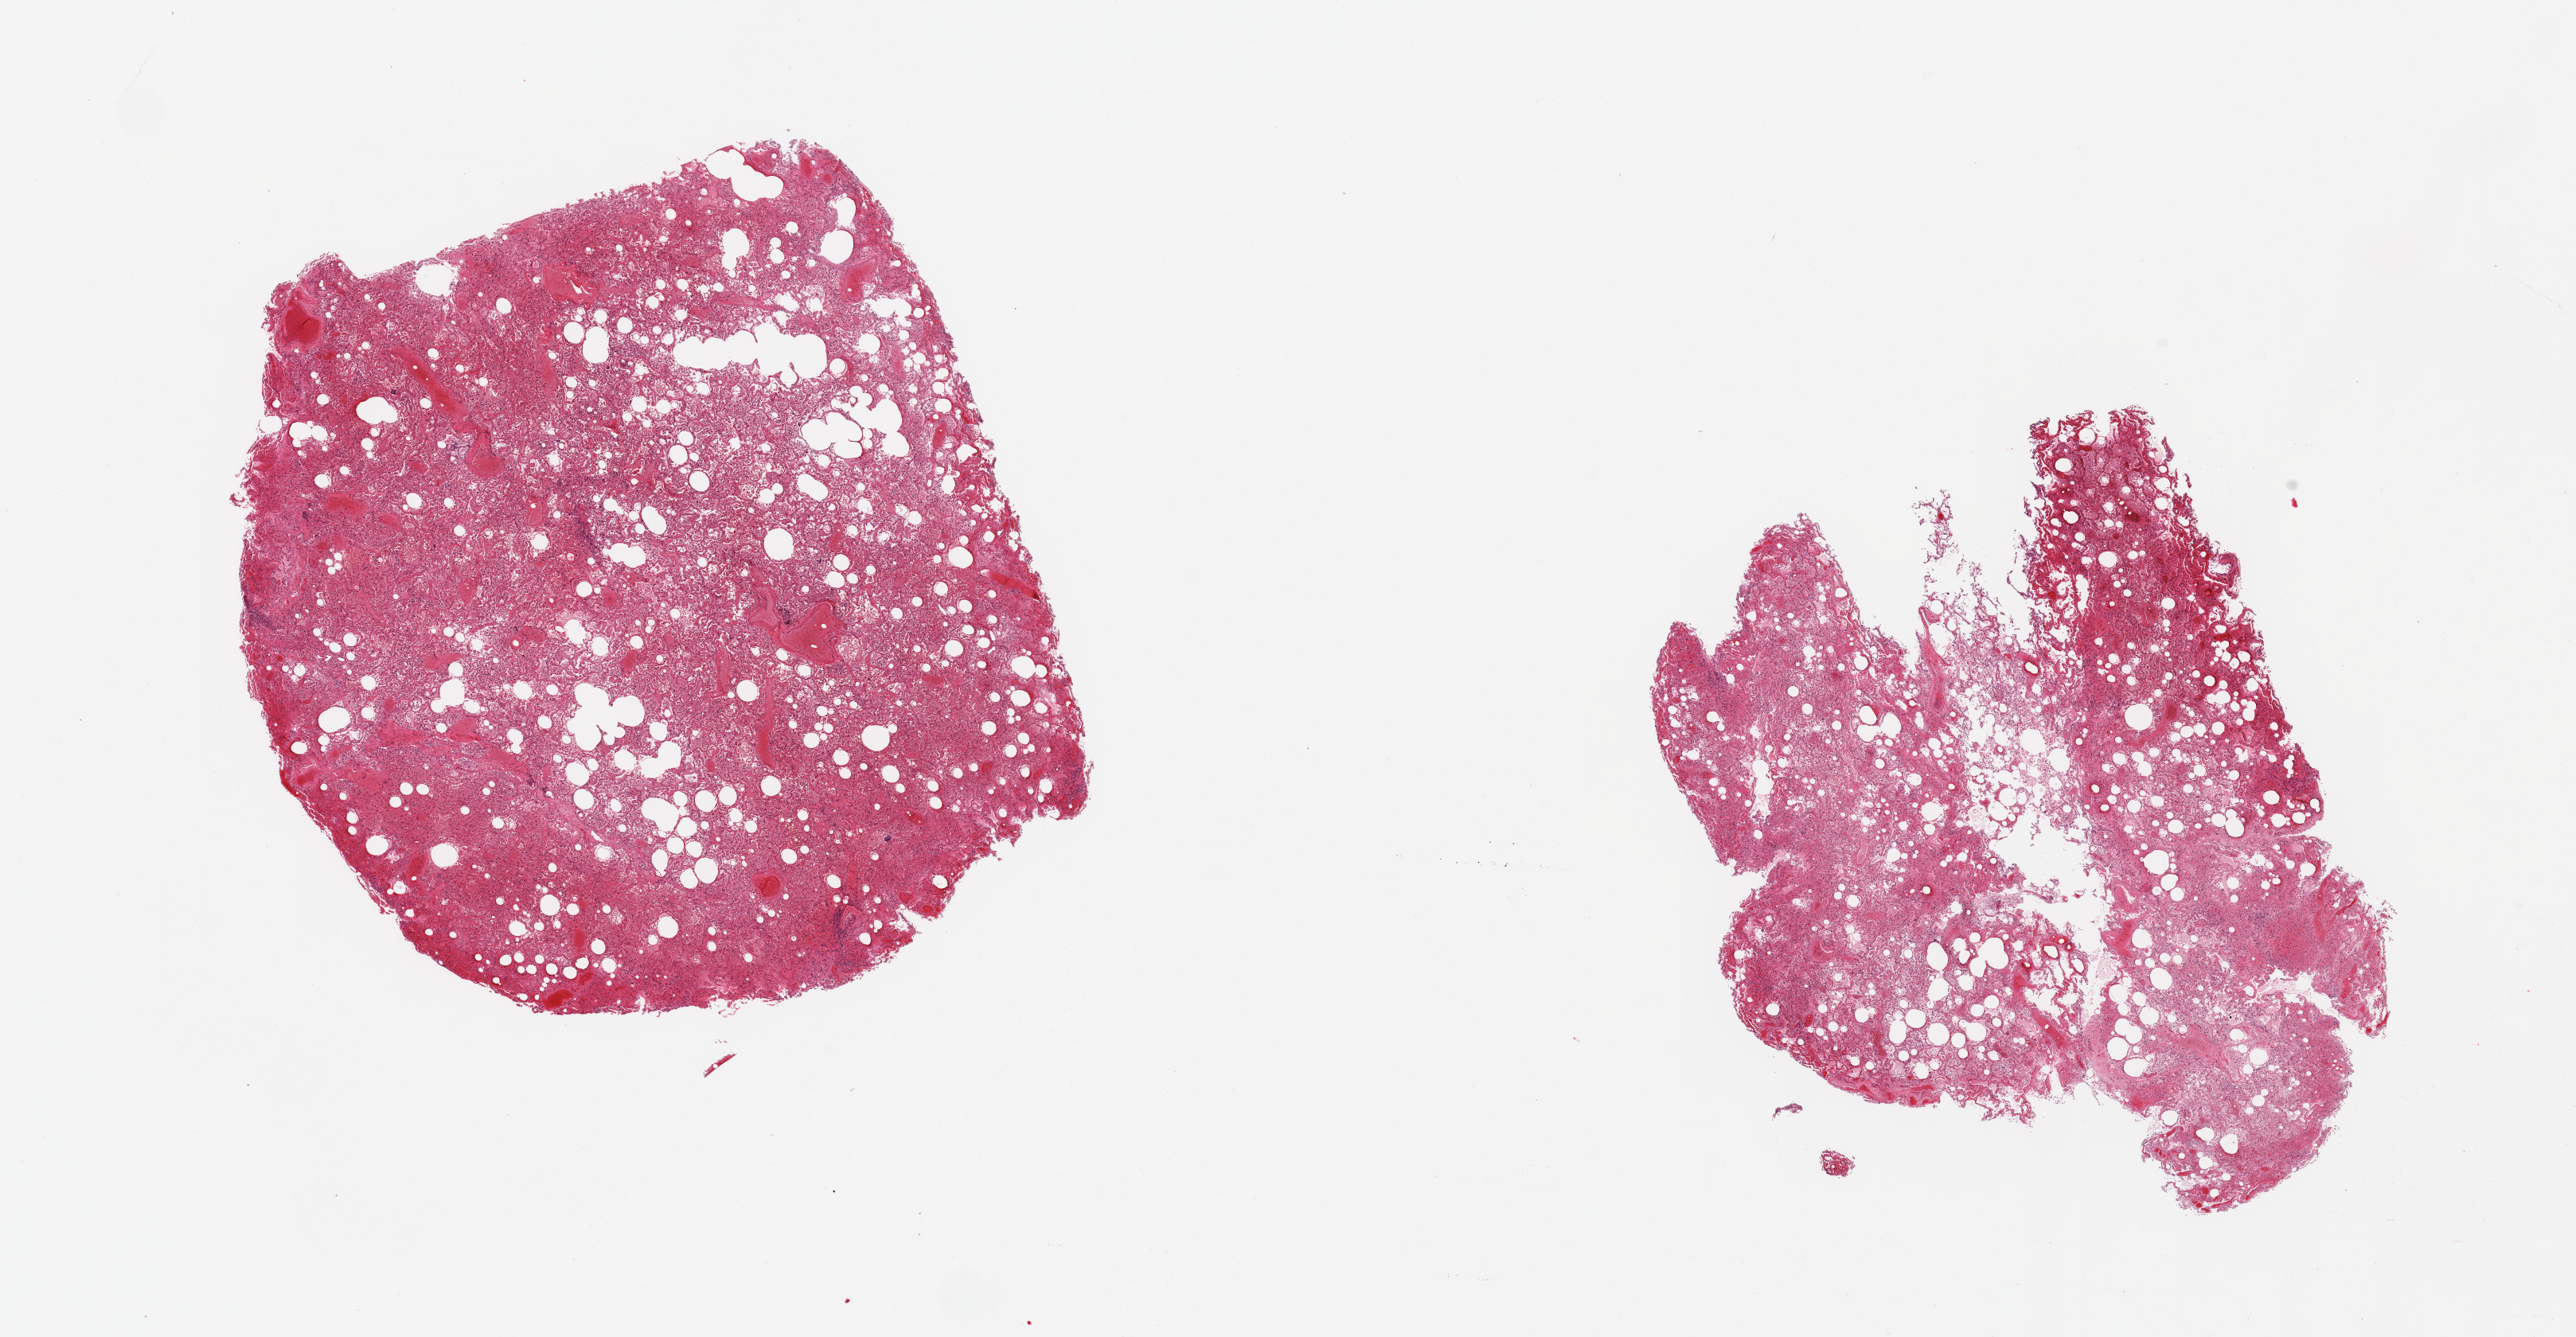
Digitized H&E-stained section — whole scanned area (about 25.6 x 13.3 mm, from a 20x scan) shown as a low-resolution overview, PAXgene-fixed, paraffin-embedded tissue, section of lung (target tissue), donor tissue sample.
• pathologist's review note for this sample: 2 pieces; congestion, intra-alveolar hemorrhage/edema